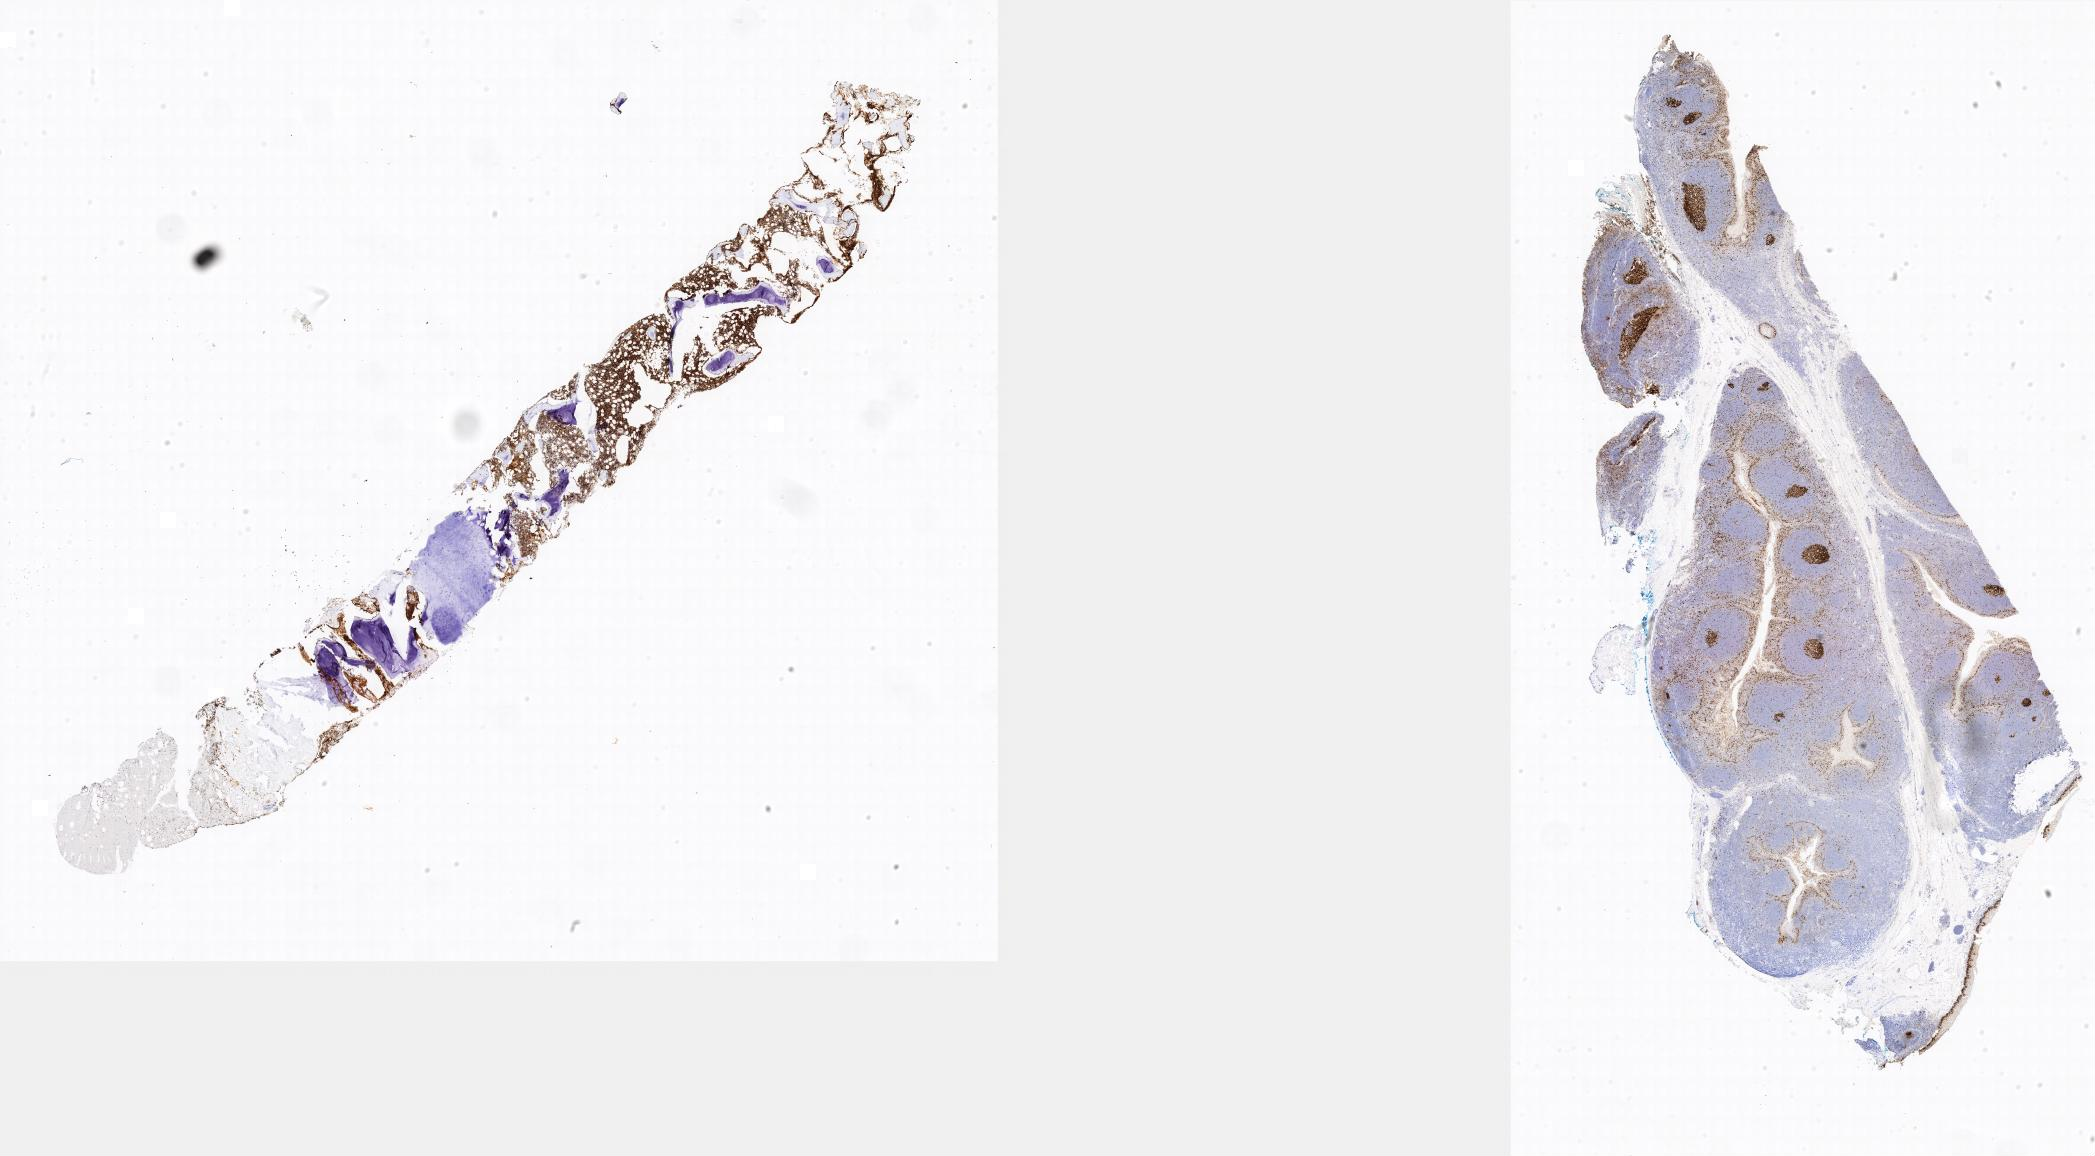
Immunohistochemistry (IHC) whole-slide image stained for Ki-67, low-resolution overview of the scanned area. Tumor tissue. Anatomic site: bone marrow. Patient male; aged 15.
Histologic diagnosis: Burkitt lymphoma, NOS.